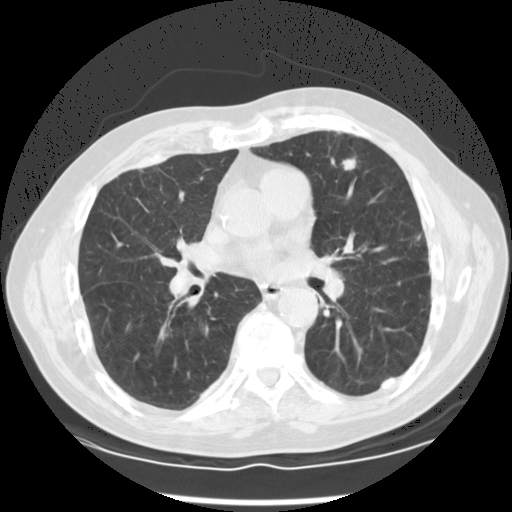
Low-dose screening chest CT, axial slice, third annual screen, lung window (W 1500 / L -600 HU), standard (soft-tissue) reconstruction kernel (STANDARD), slice 65 of 120 in the series. Male, age 68 years at enrolment. Former smoker at enrolment.
Lesion marked by an expert reader, box from (x=324, y=148) to (x=371, y=191) px. The exam's reader record, not a measurement of the box and not confirmed to be the same lesion: non-calcified nodule or mass ≥4 mm, left upper lobe, 10 × 8 mm, spiculated (stellate) margins, soft tissue attenuation, pre-existing on the prior screen: no. Later outcome: lung cancer diagnosed 53 days after this screen — squamous cell carcinoma, NOS, left upper lobe, moderately differentiated (G2), stage IA (AJCC 6th edition), 17 mm at pathology.